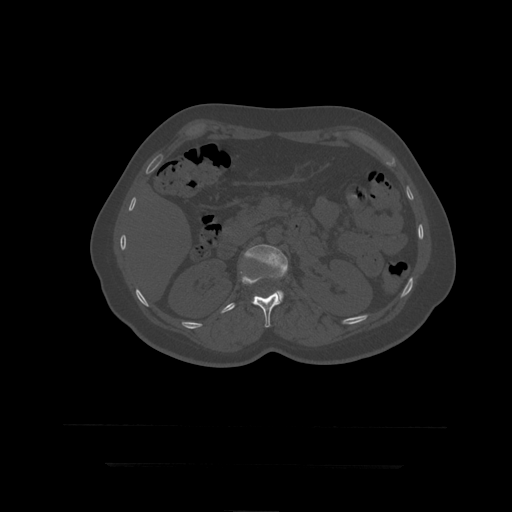
CT including the spine, one axial slice. Position 165 of 399 along the scan axis. Reconstruction kernel STANDARD. 120 kVp. Bone window (W 1800 / L 400 HU). 1.25 mm slice thickness. 512 × 512 image matrix, field of view 450 × 450 mm. Patient age 41 years. From the clinical record (not read from this slice): primary cancer: breast.
Annotated regions visible in this slice (semi-automatically segmented with operator editing):
- L1 vertebra: bounding box <241,272,281,328> (left, top, right, bottom; pixels)
- L2 vertebra: <244,245,288,302>